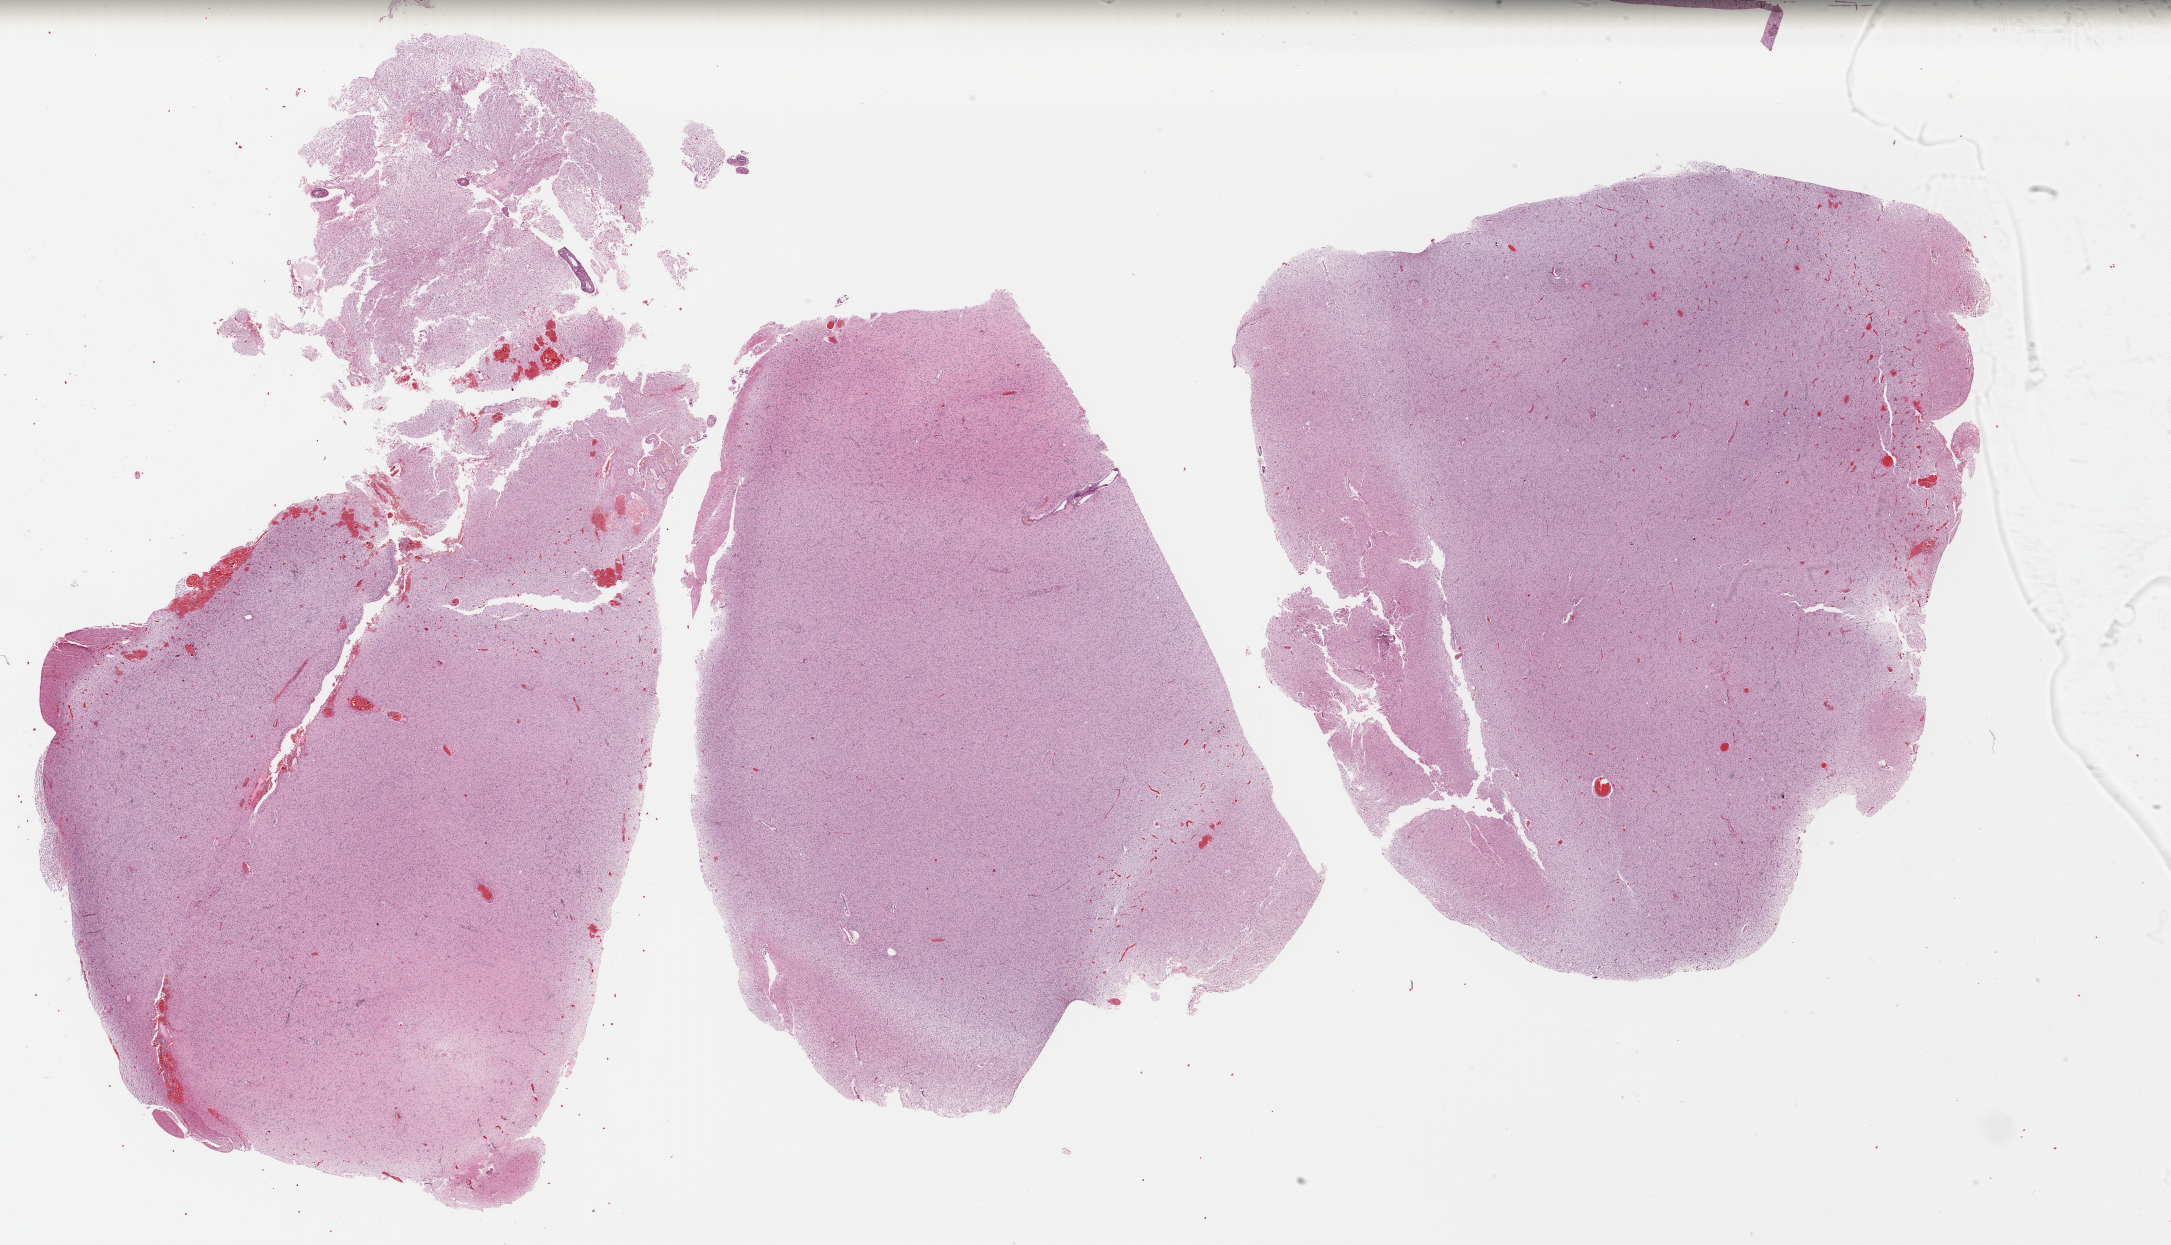
Whole-slide histology image, H&E — whole scanned area (about 34.1 x 19.6 mm, slide scanned at 40x) shown as a low-resolution overview, formalin-fixed paraffin-embedded (FFPE) diagnostic section, brain, primary tumour sample. Male, age 36 years at initial diagnosis. Histologic grade: G3 (poorly differentiated).
Pathologic diagnosis: Astrocytoma, anaplastic (cerebrum). Laterality: right.